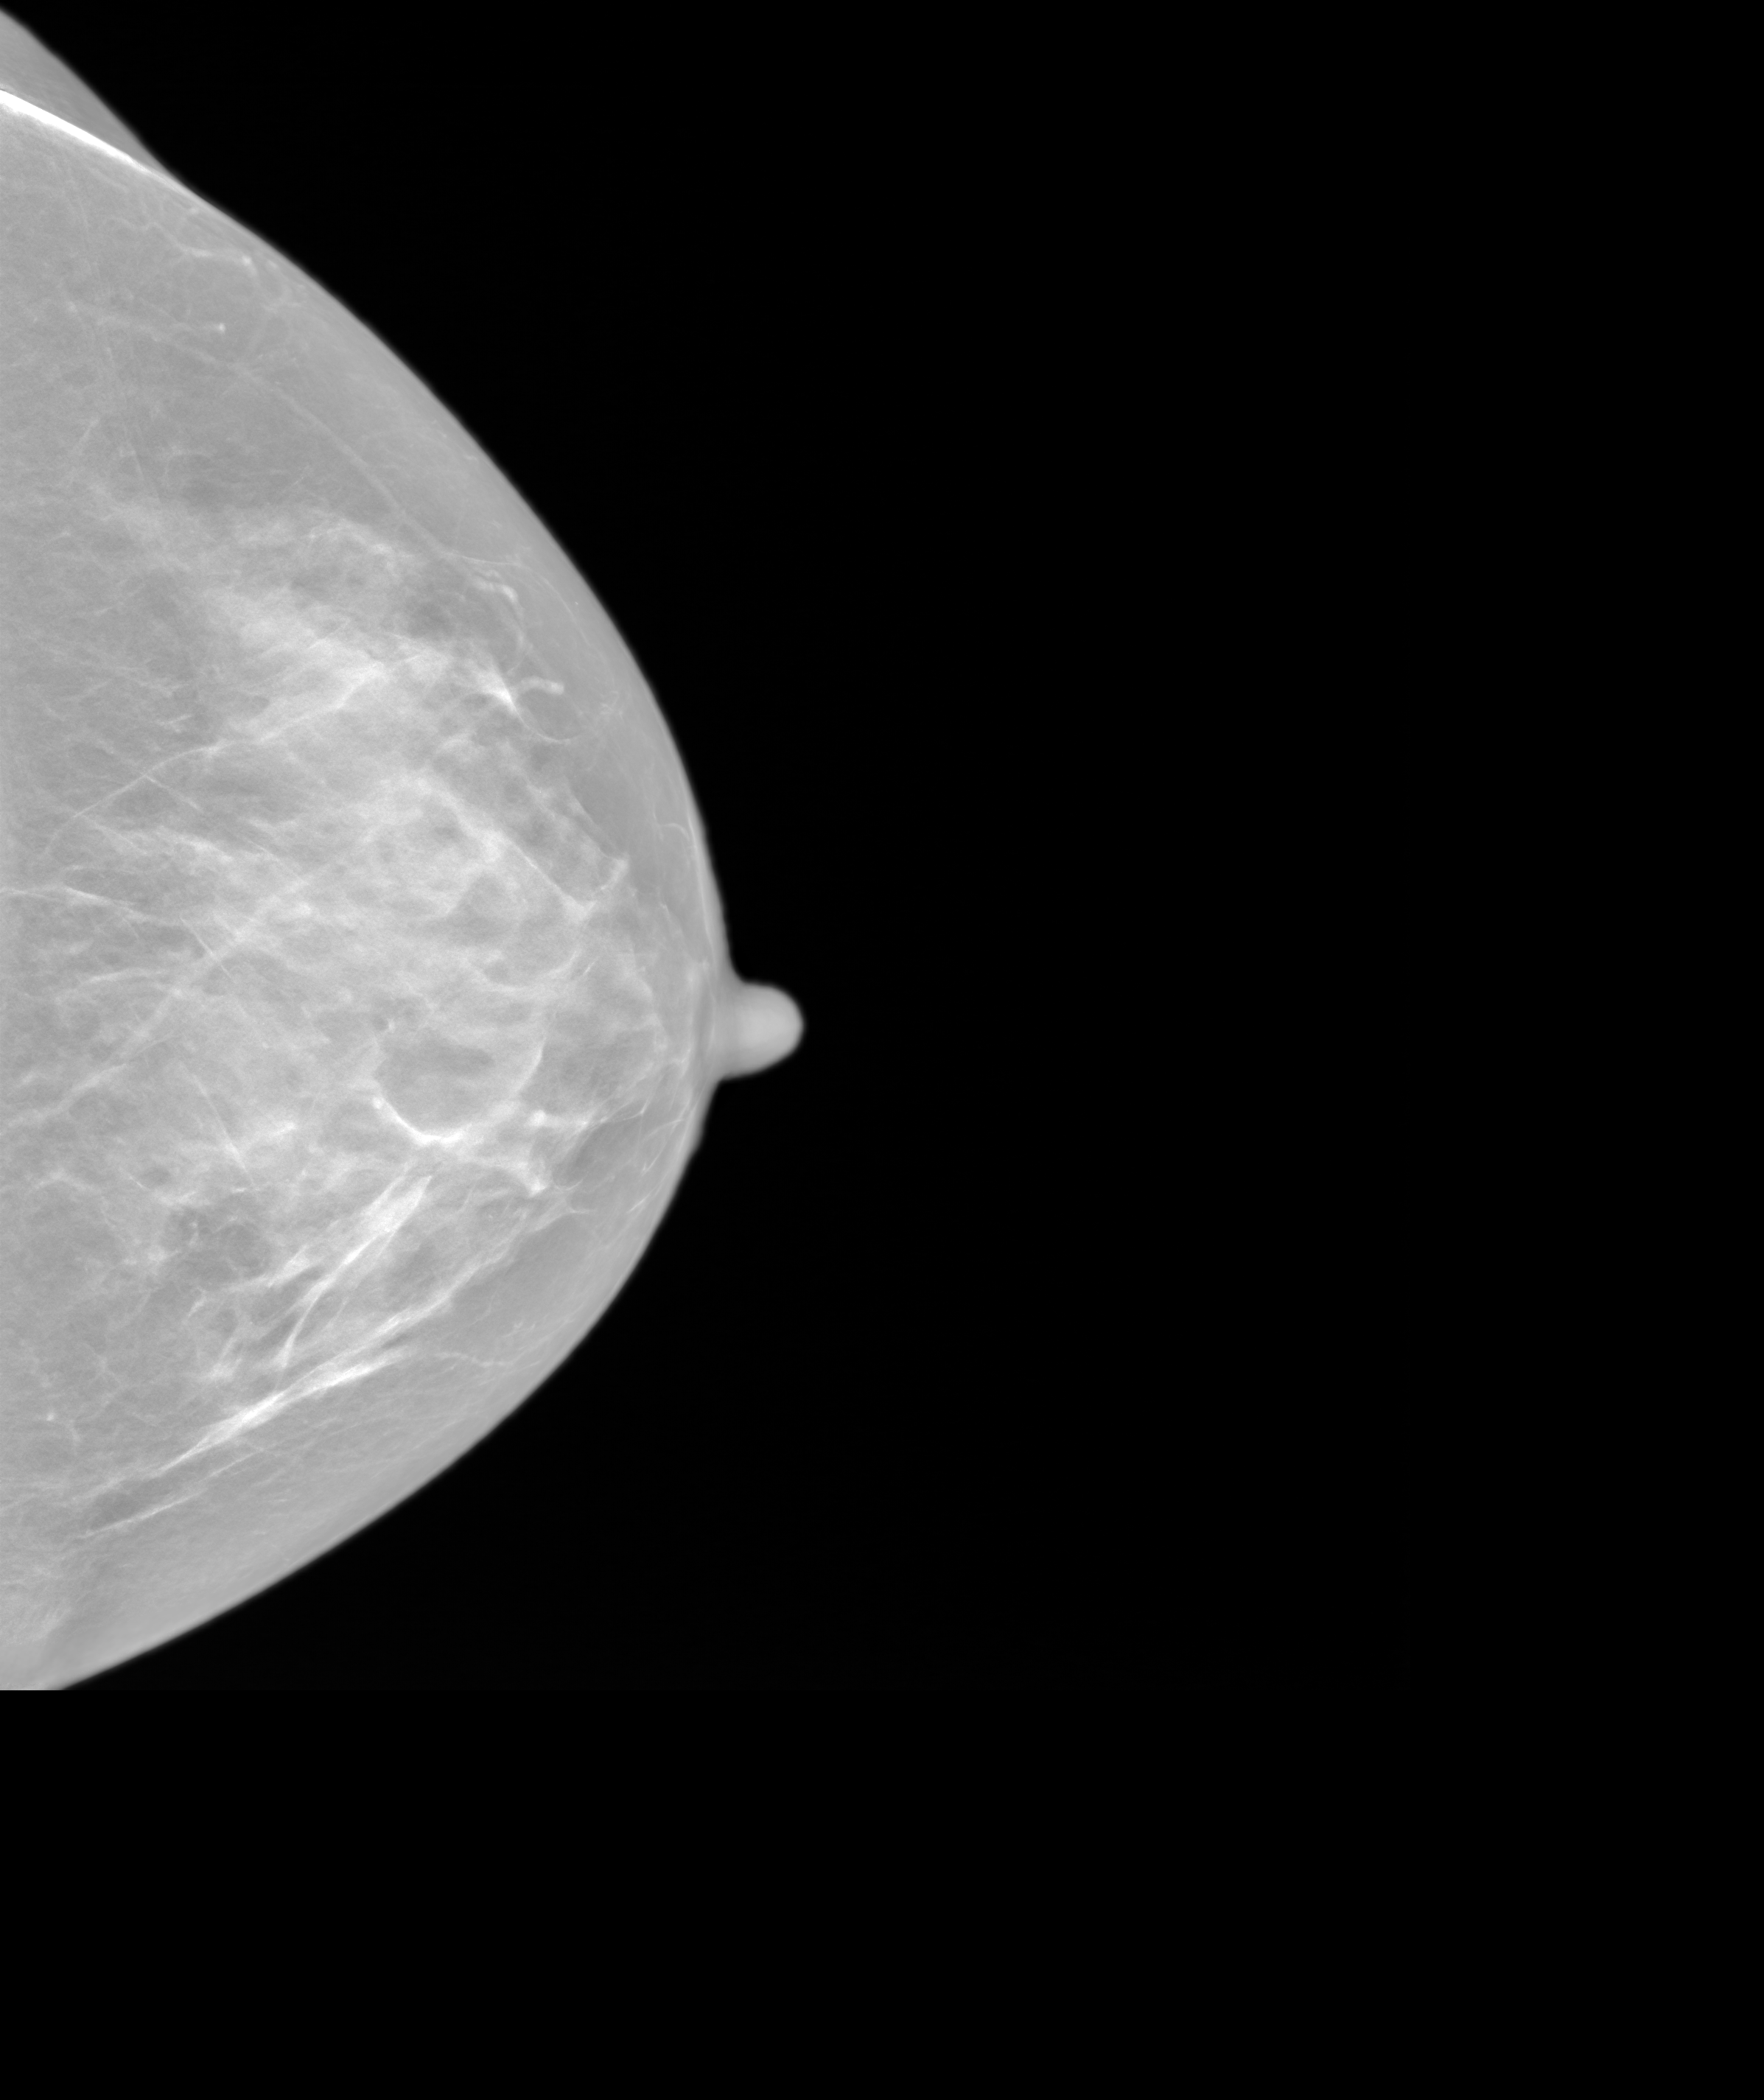
Annual screening mammography examination; system: SenoIris_1SP2(440). Female patient, age 68 years.
Image type: synthesized 2-D view from tomosynthesis. Breast: left. Projection: craniocaudal (CC) view.